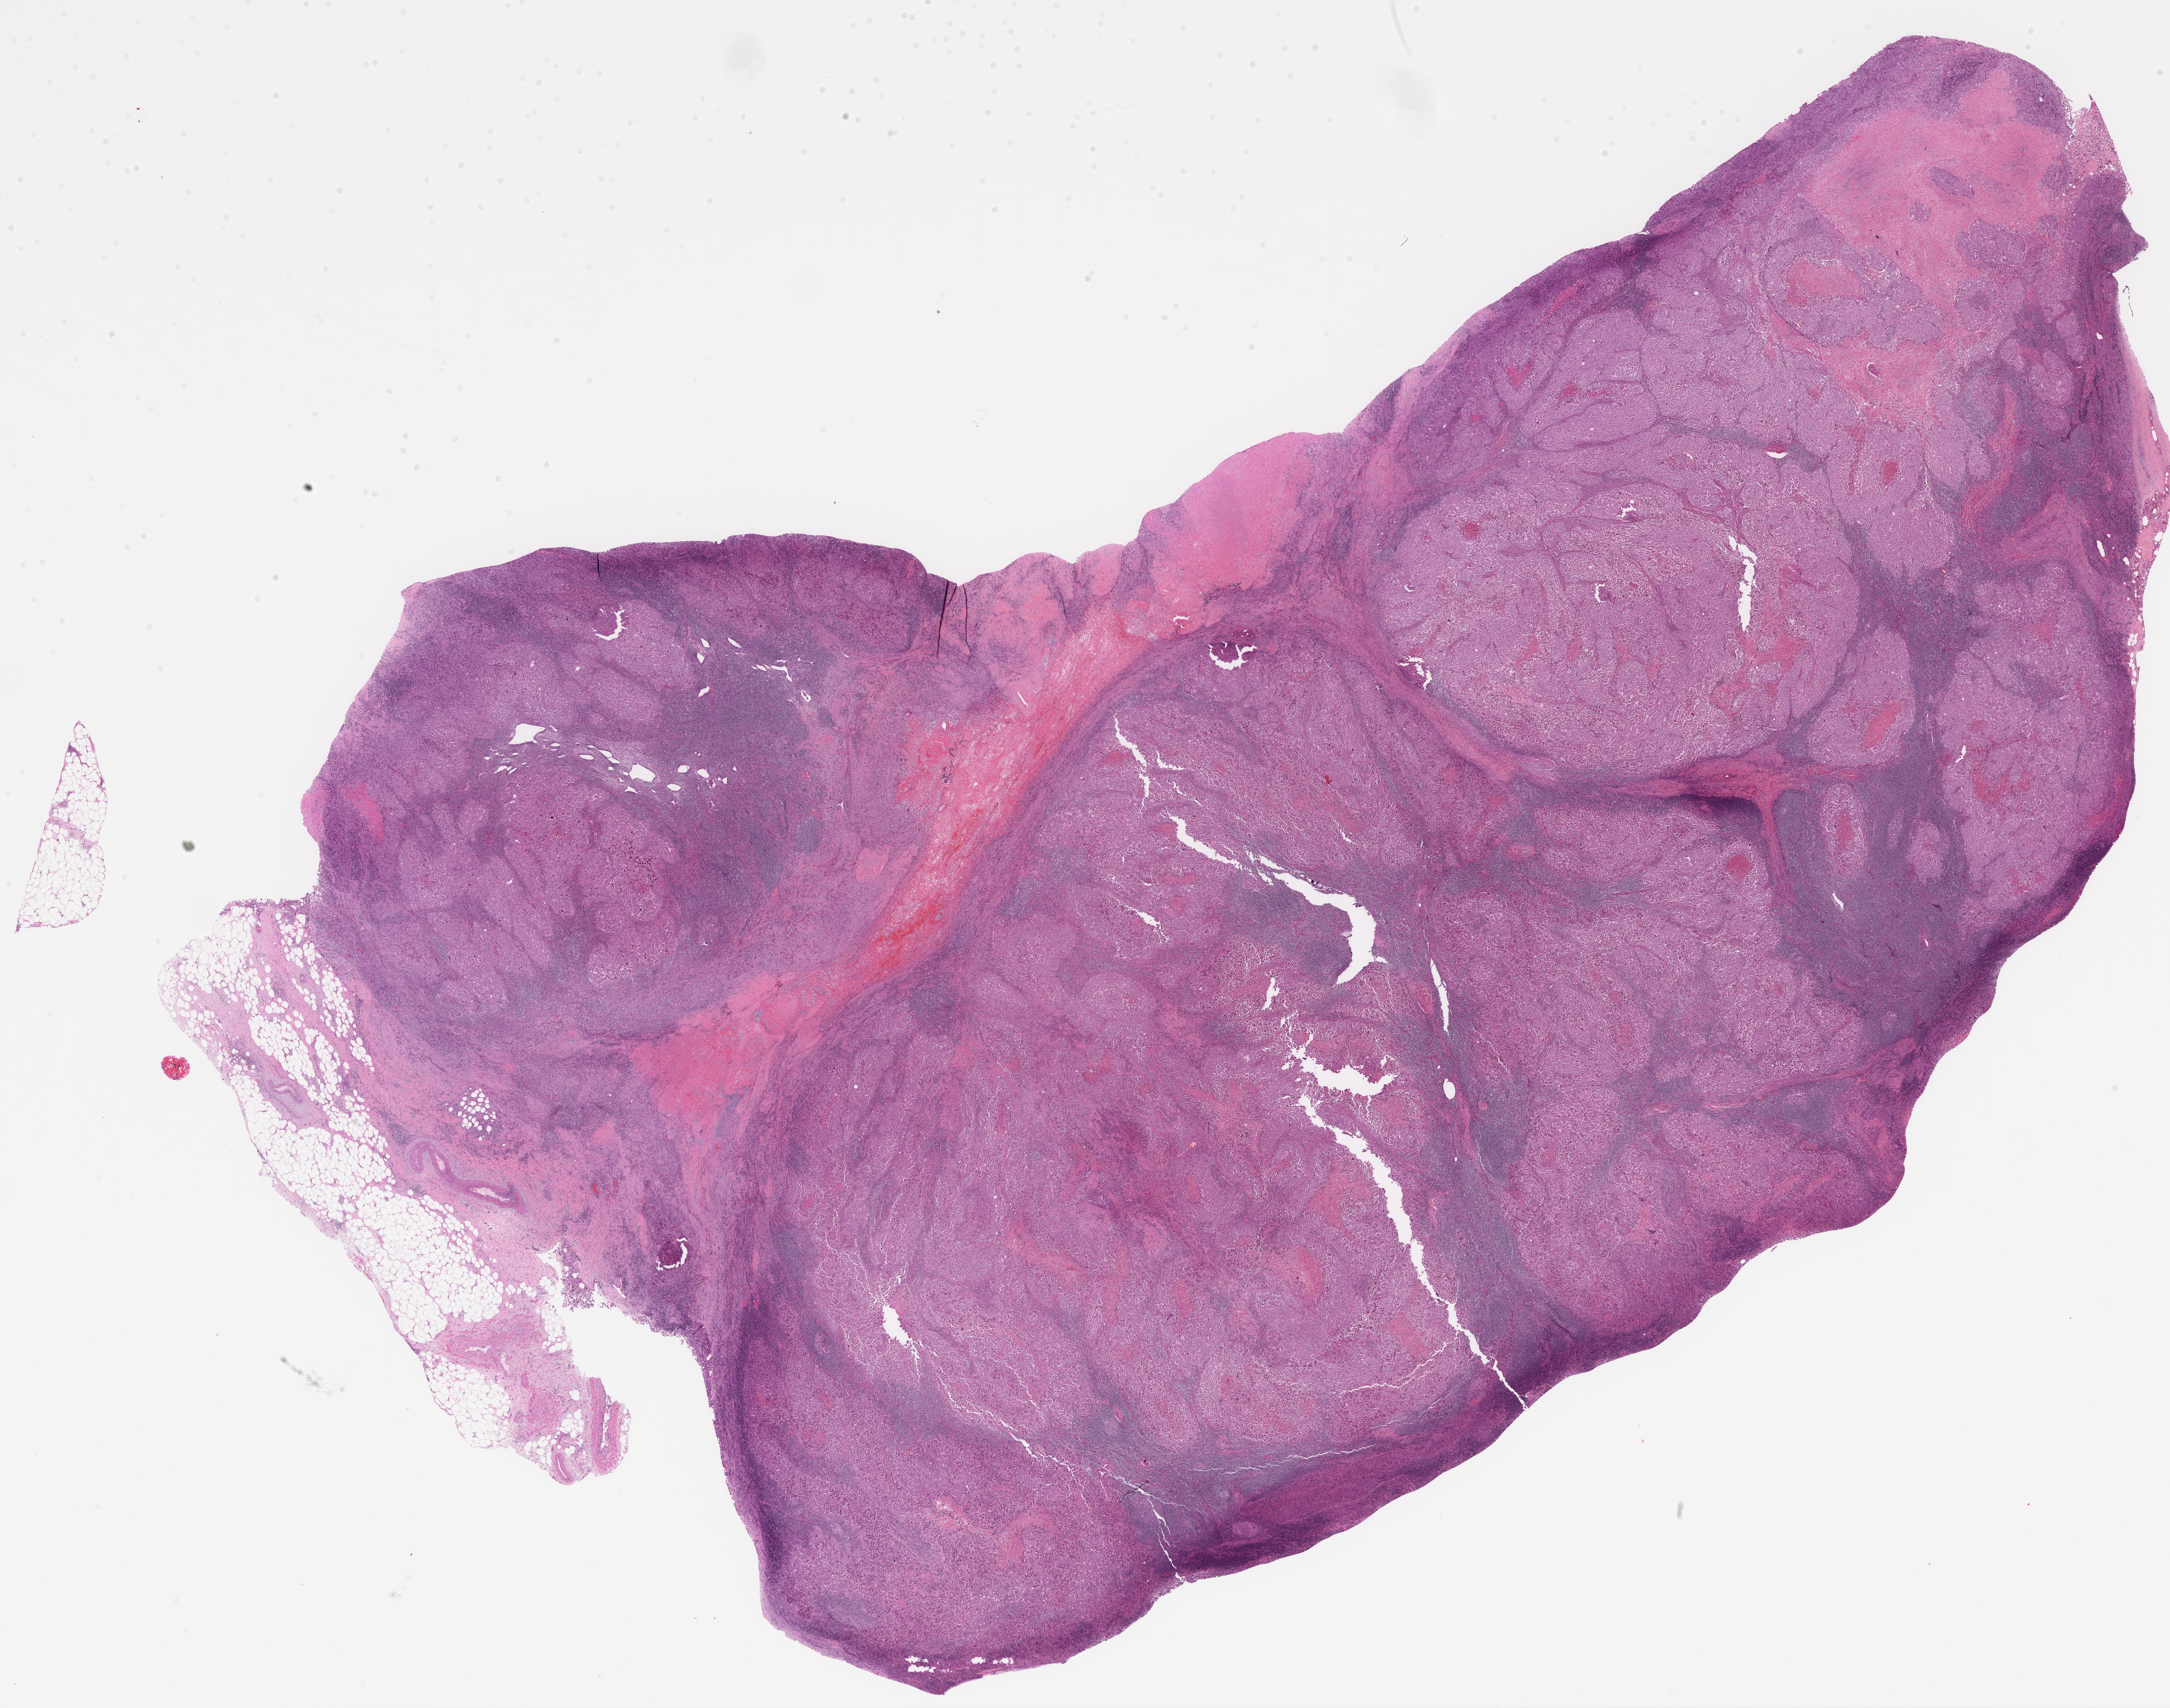
Whole-slide histology image, H&E — a low-resolution overview of the entire scanned area, about 26.9 x 21.2 mm; formalin-fixed paraffin-embedded (FFPE) diagnostic section; metastatic tumour sample, sampled site not recorded. Female patient; age at initial diagnosis 23 years.
• this section: metastatic tumour tissue
• patient diagnosis: Malignant melanoma, NOS